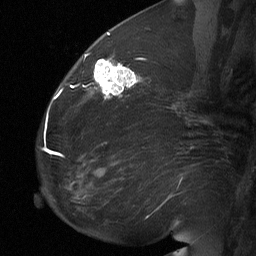
Breast MRI (dynamic contrast-enhanced), one sagittal slice. Dynamic contrast-enhanced study with each time point stored as its own series, time point 2 of 3 at this slice position (early post-contrast, ordered by acquisition time). 1.5 T. TE 4.8 ms, TR 27 ms. 256 × 256 image matrix, field of view 200 × 200 mm. Patient: female, 60 years. From the clinical record (not read from this slice): setting: breast cancer imaged before/during neoadjuvant chemotherapy; receptor status: HR-positive, HER2-negative.
Outlined on this slice (semi-automatically segmented with operator editing):
- analysis volume of interest (the breast-tissue region the enhancement analysis was run in; not a lesion): box from (x=91, y=56) to (x=139, y=103) px
- tumour enhancement mask (voxels above the 90 % enhancement threshold inside the analysis volume of interest): (x=94, y=59)–(x=139, y=98)